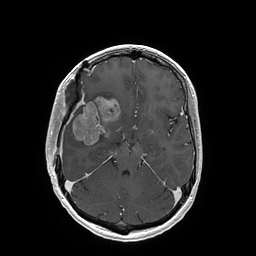
Brain MRI from a brain-tumour surgery series, one axial slice; position 106 of 202 along the scan axis; T1-weighted post-contrast; 1 mm slice thickness; 256 × 256 image matrix, field of view 250 × 250 mm. From the clinical record (not read from this slice): histopathology: Glioblastoma; WHO grade: 4; IDH mutation: no; tumour location: Right Insular.
Structures marked on this image (expert manual segmentation):
- tumour: bounding box [x1, y1, x2, y2] px = [72, 97, 120, 146]